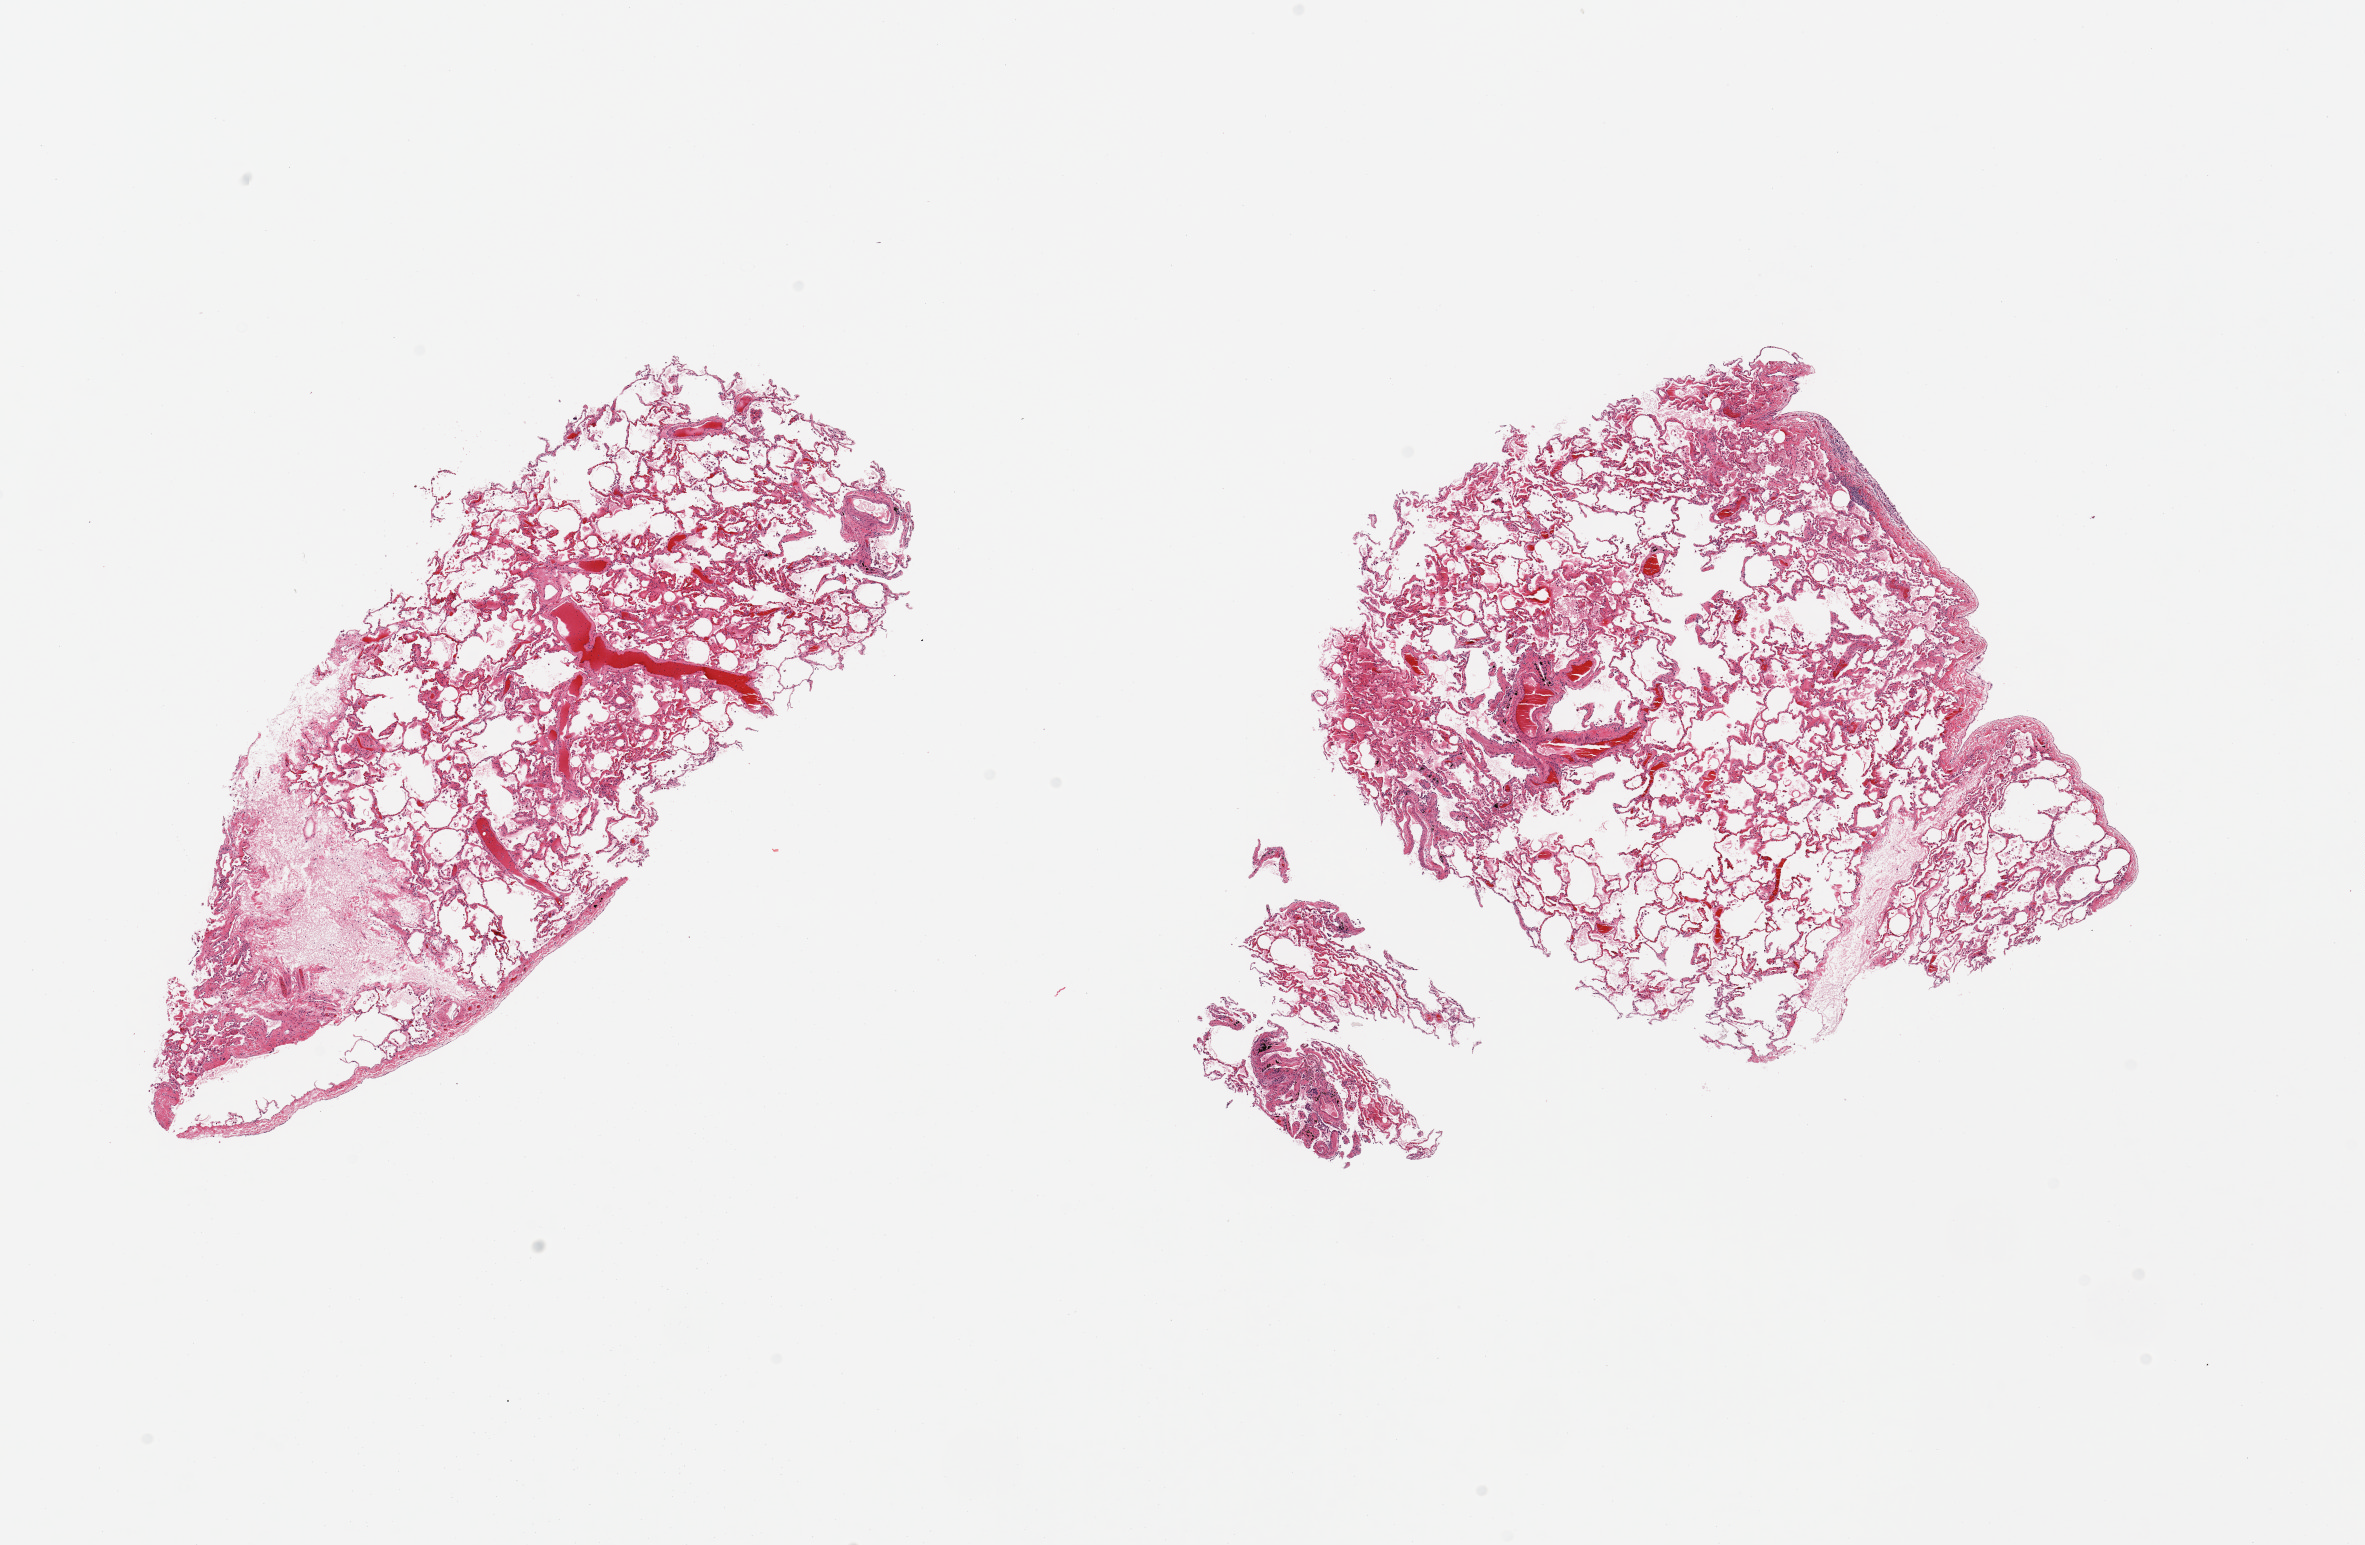
Digitized hematoxylin and eosin (H&E)-stained section — a low-resolution overview of the entire scanned area, about 18.7 x 12.2 mm. PAXgene-fixed paraffin-embedded (PFPE) section. Sampled site (target tissue): lung. Tissue donor sample. Male donor.
Reviewer comment on this tissue sample: 2 pieces; emphysema.